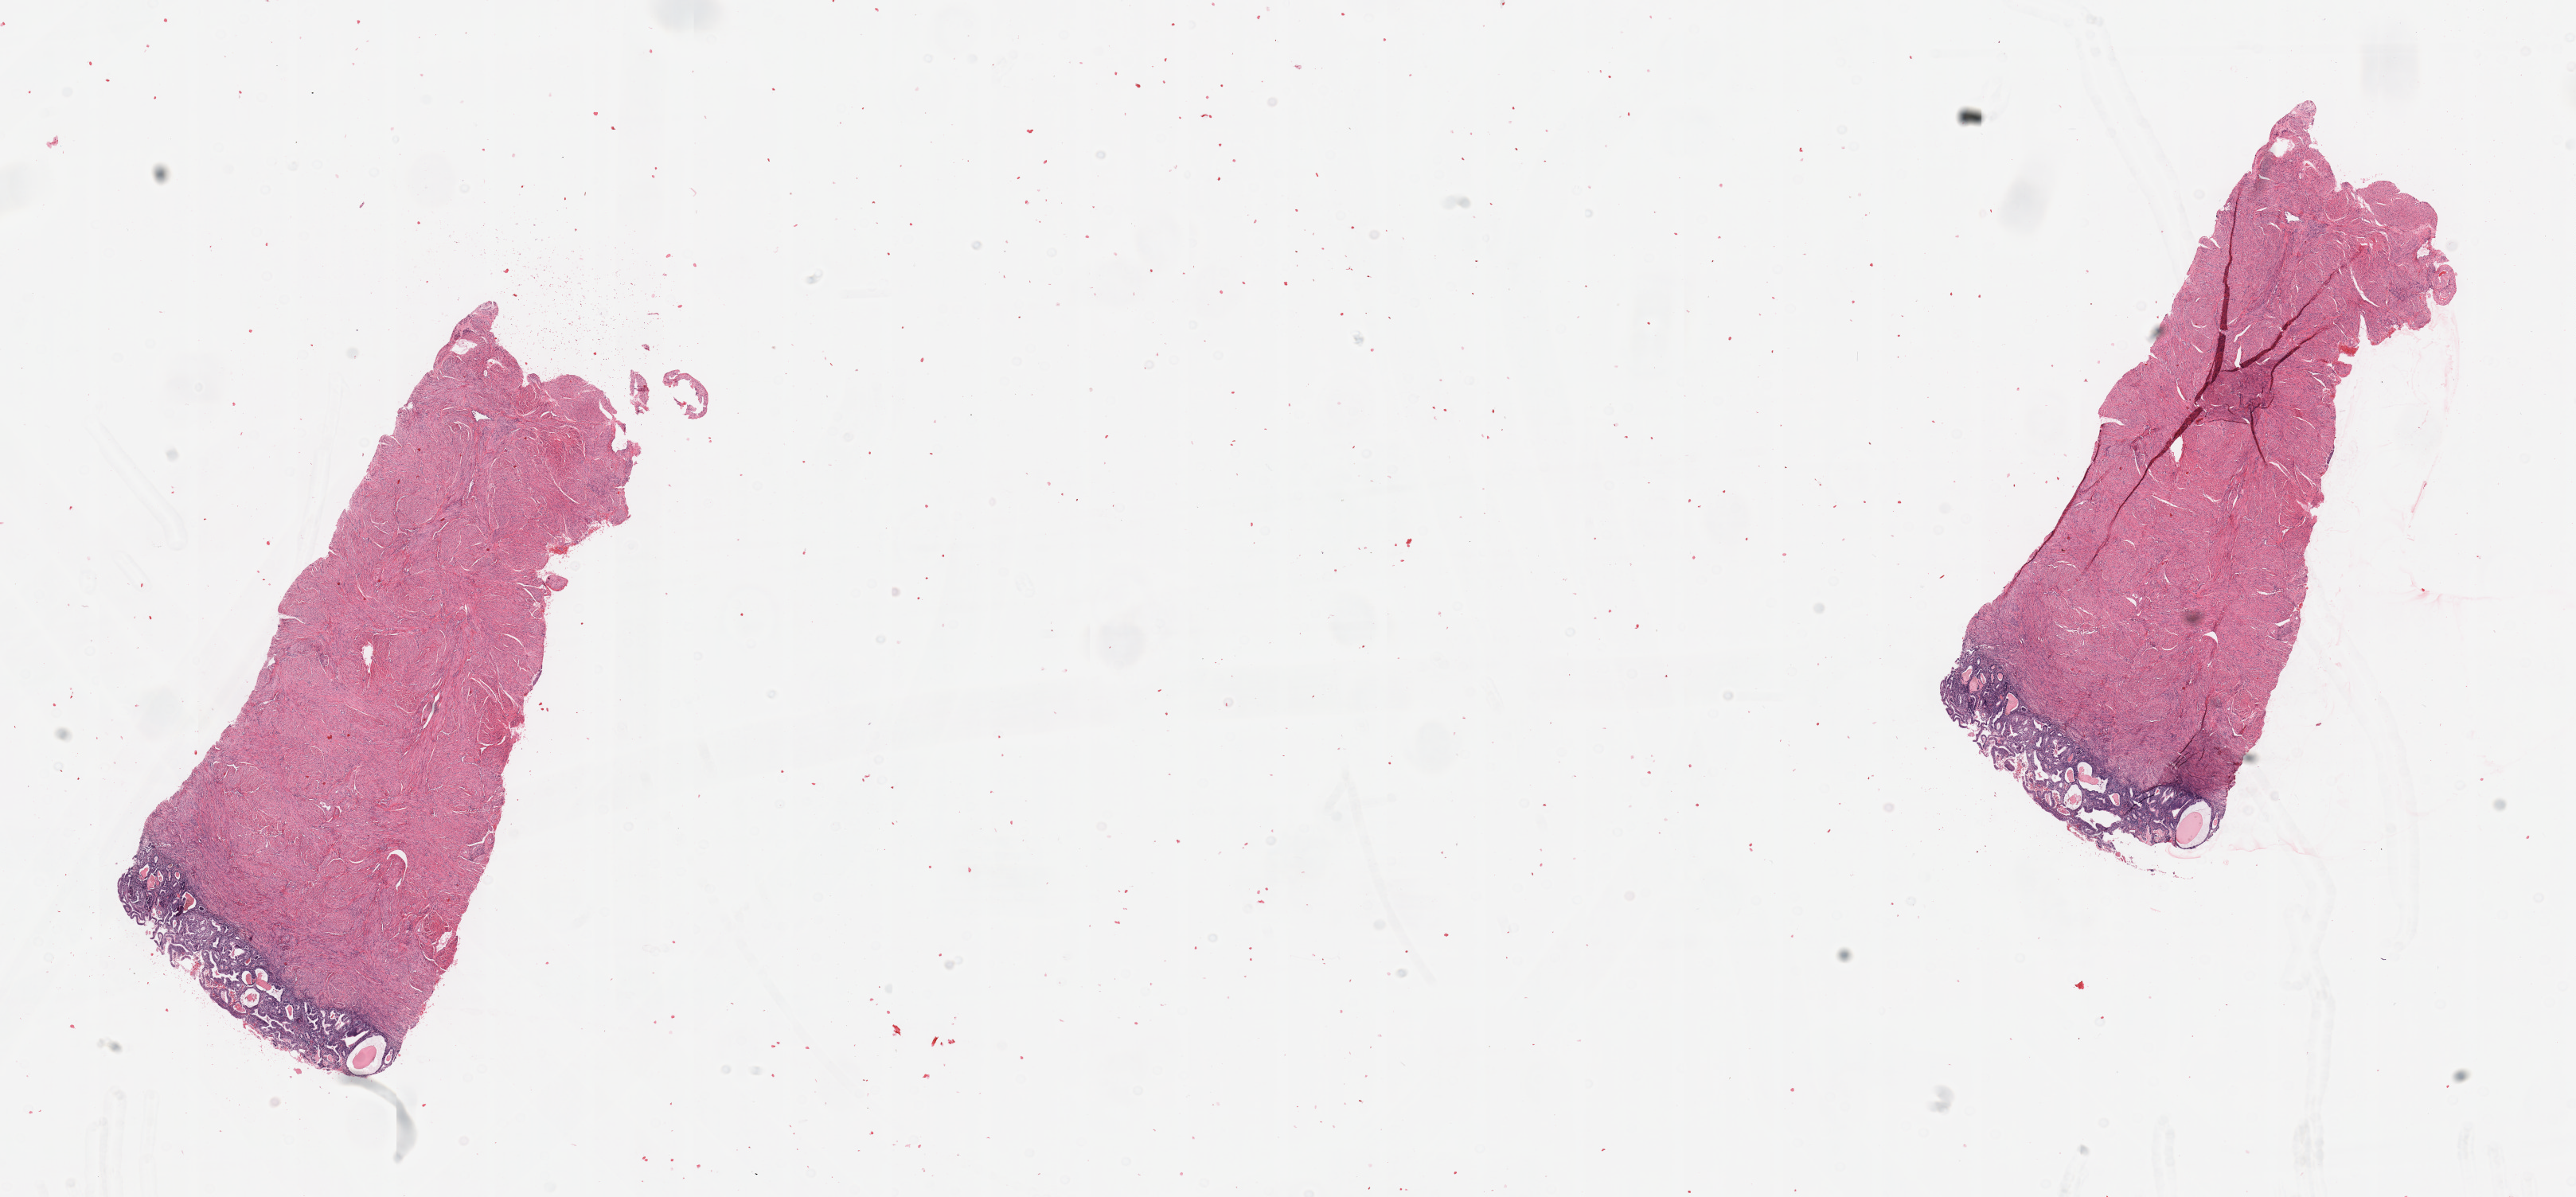
Hematoxylin and eosin (H&E) stained whole-slide image, whole scanned area (about 25.6 x 11.9 mm) shown as a low-resolution overview. Normal (non-tumour) tissue sample, sampled site: uterus. Patient: female, age 51 years.
This section: normal (non-tumour) tissue from the same patient. Patient diagnosis: Endometrioid adenocarcinoma, NOS.